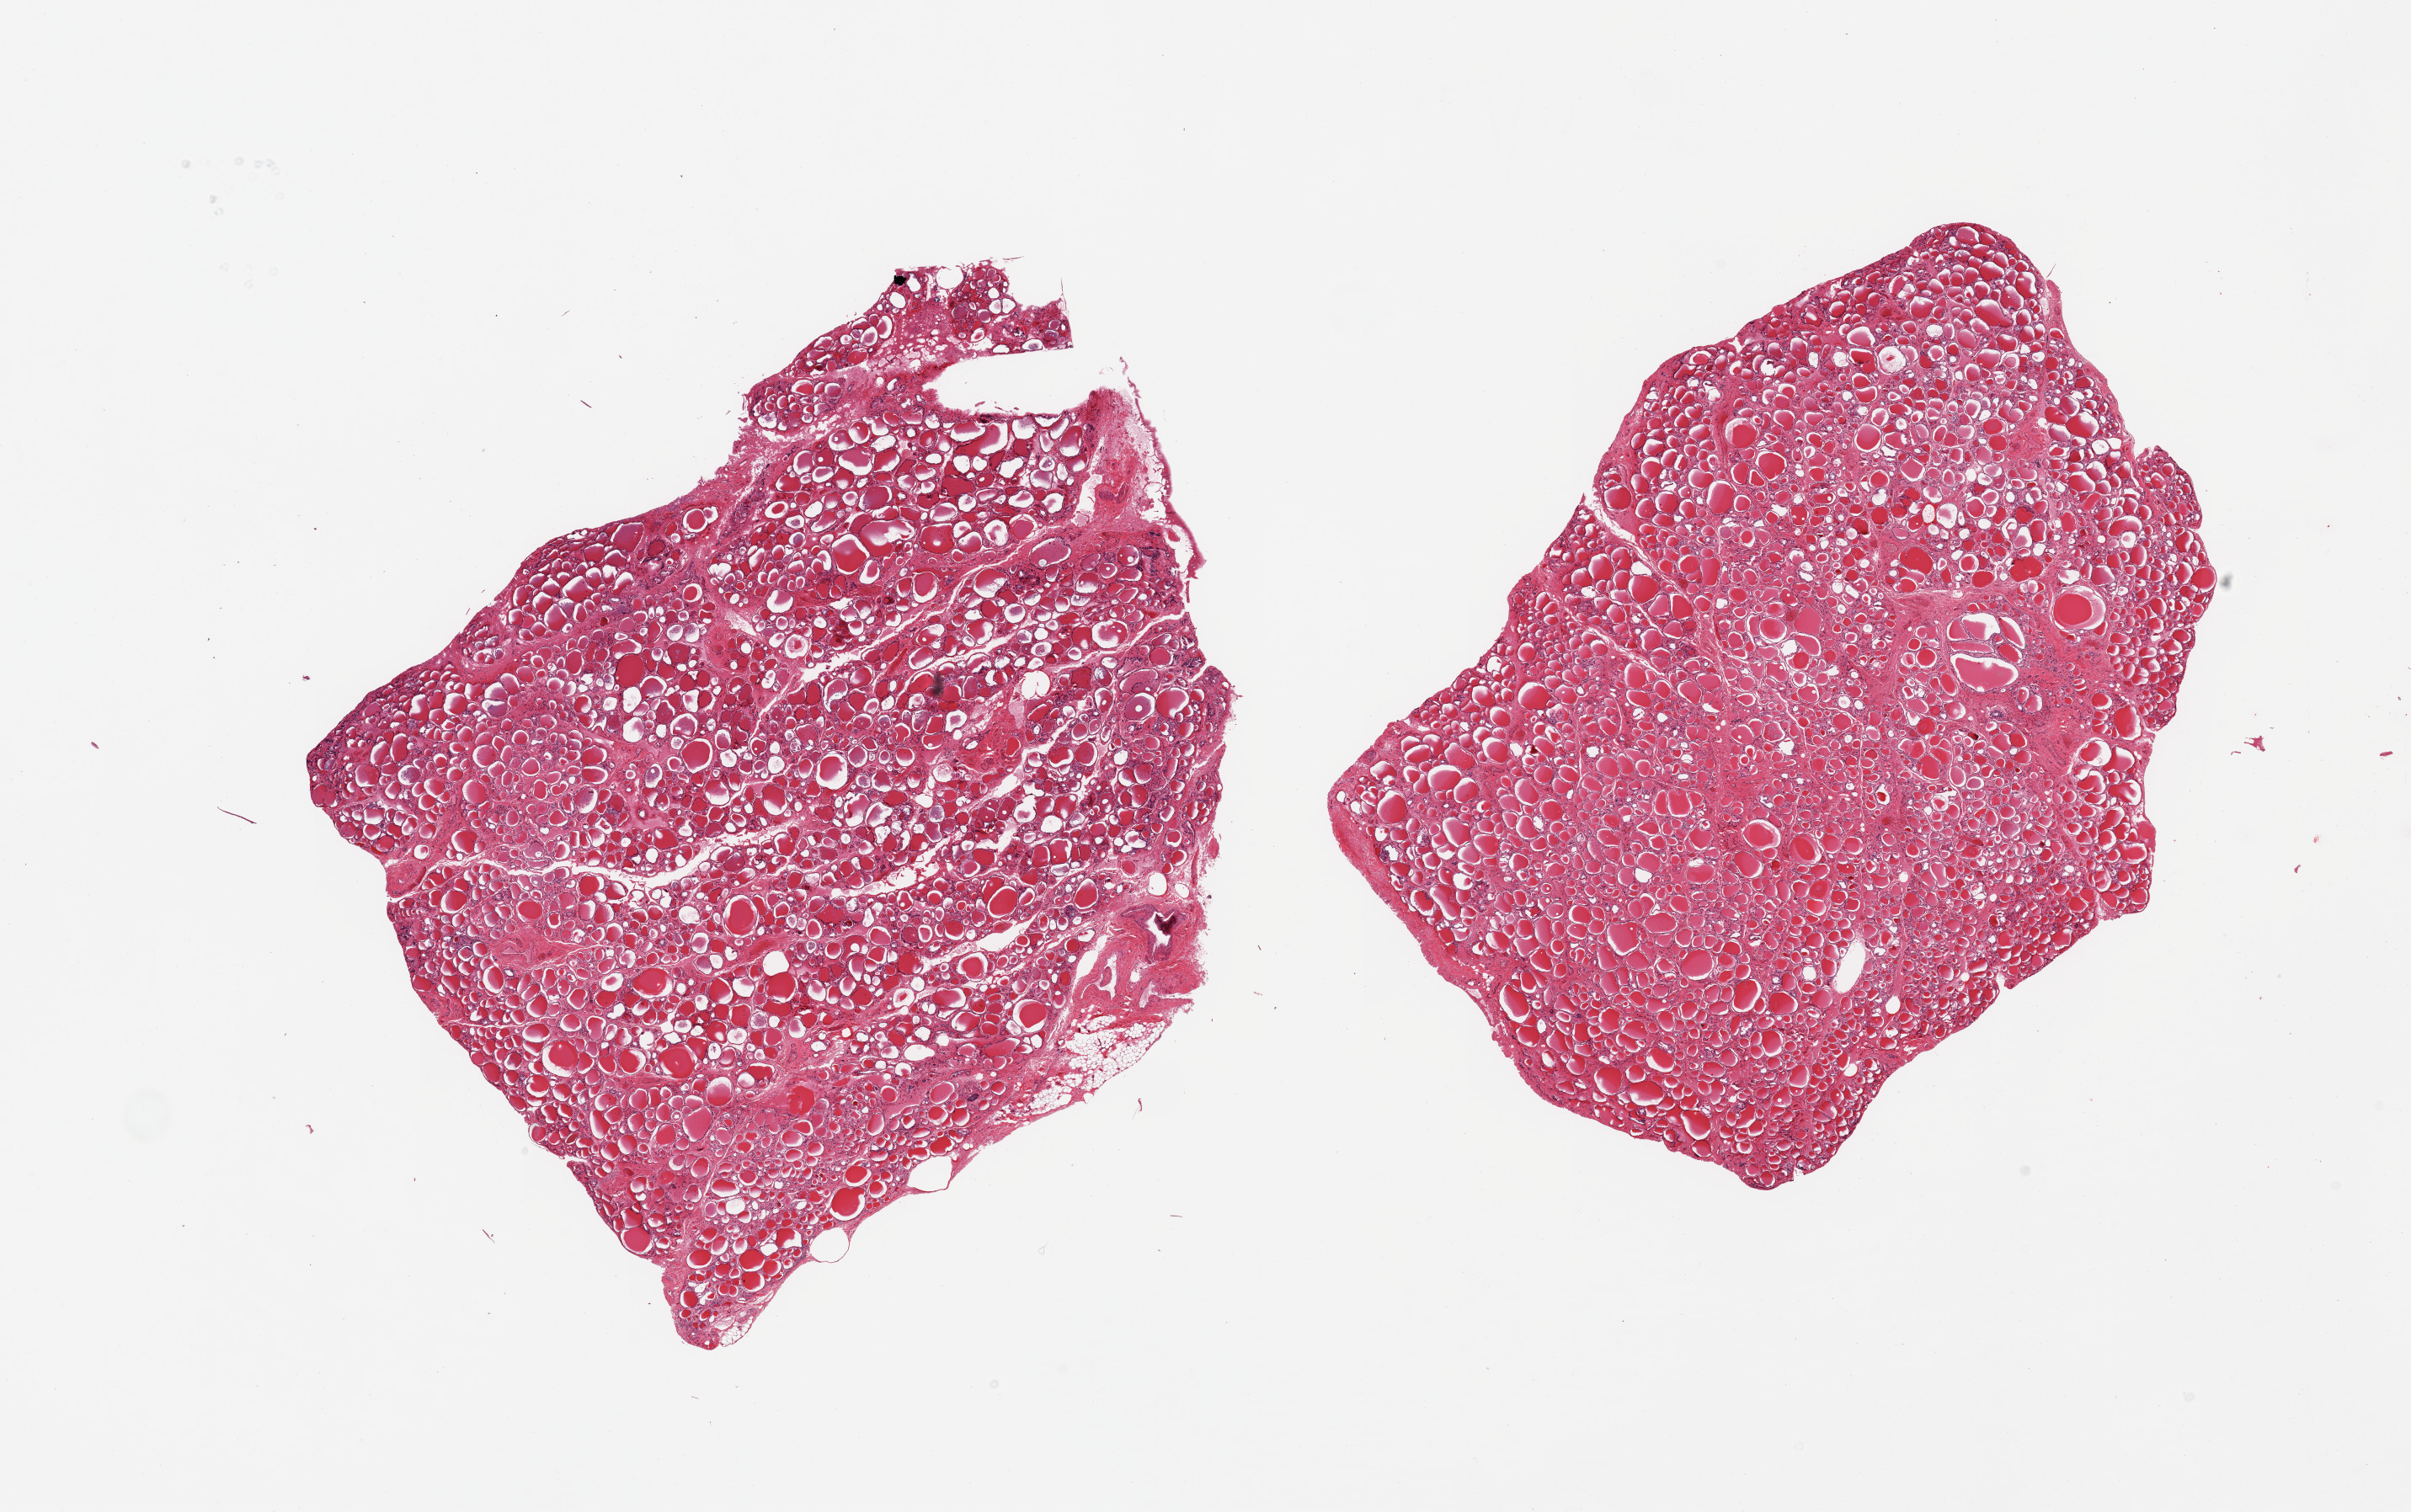
Digitized H&E-stained section, low-resolution overview of the scanned area, about 22.6 x 14.2 mm. PAXgene-fixed paraffin-embedded (PFPE) section. Target tissue: thyroid. Tissue donor sample. Donor sex: female.
Pathologist's review note for this sample: 2 pieces; no lesions.